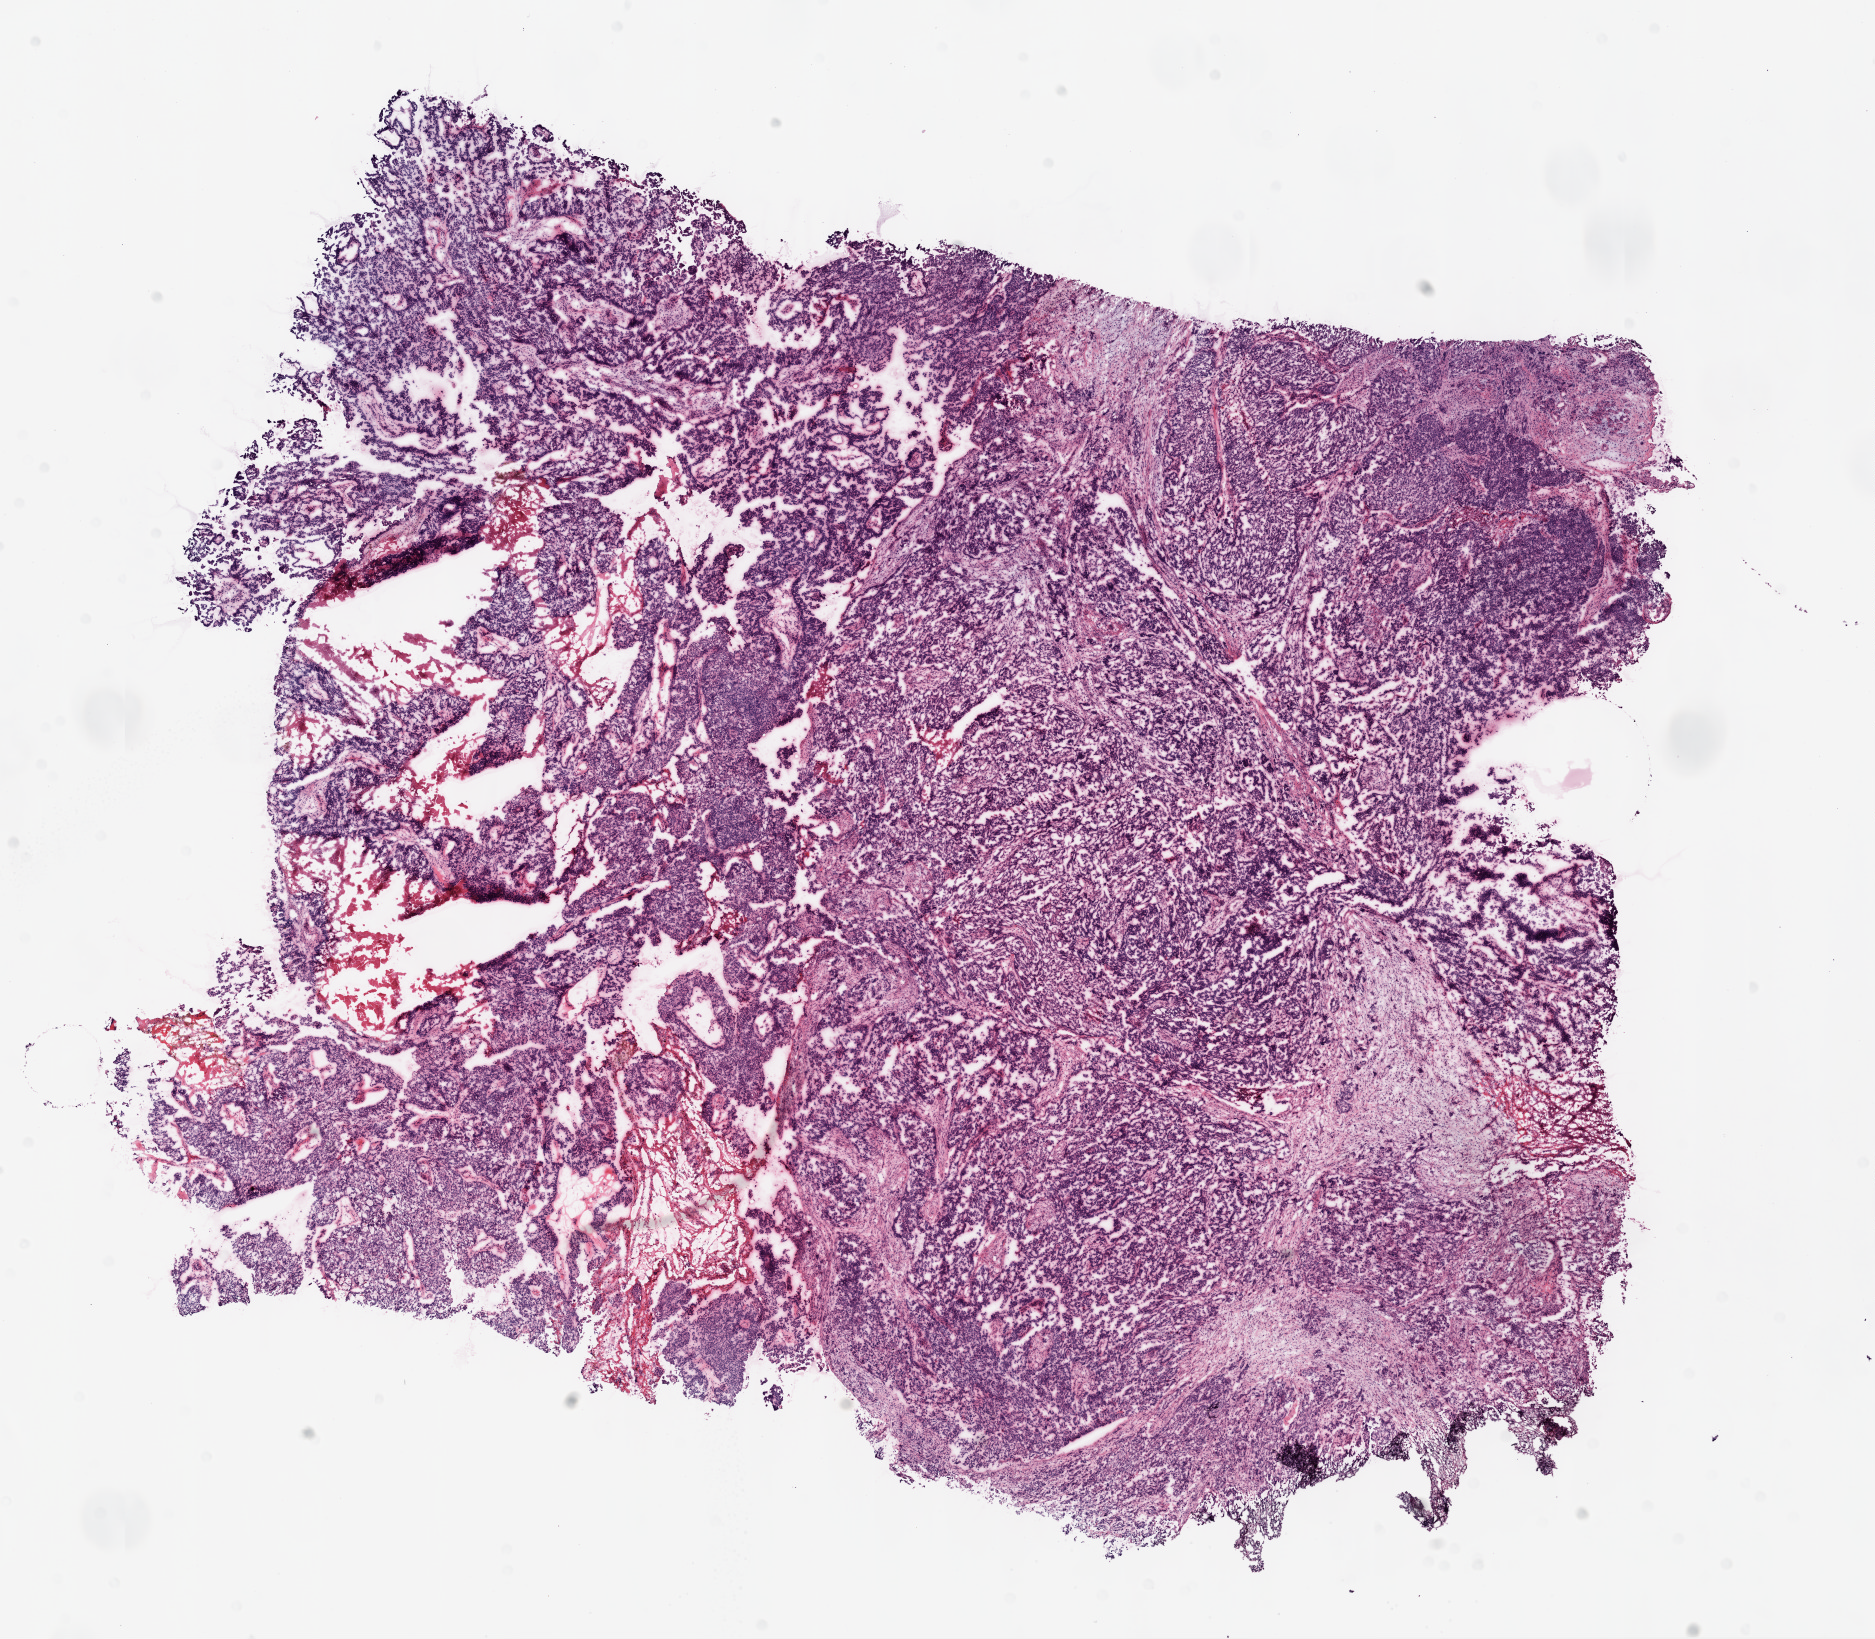
Digitized Hematoxylin and eosin (H&E) stained tissue section (whole slide) — low-resolution overview of the scanned area, about 15.0 x 13.2 mm (acquisition: 20x scan), frozen section from the top of the tissue portion, ovary, primary tumour sample. Female, age 48 years at initial diagnosis. Histologic grade: G3 (poorly differentiated). Pathologist review of this section (percent, as recorded): tumour cells 85%, tumour nuclei 90%, normal cells 0%, stromal cells 10%, necrosis 5%.
FIGO stage: IIIC. Pathologic diagnosis: Serous cystadenocarcinoma, NOS.